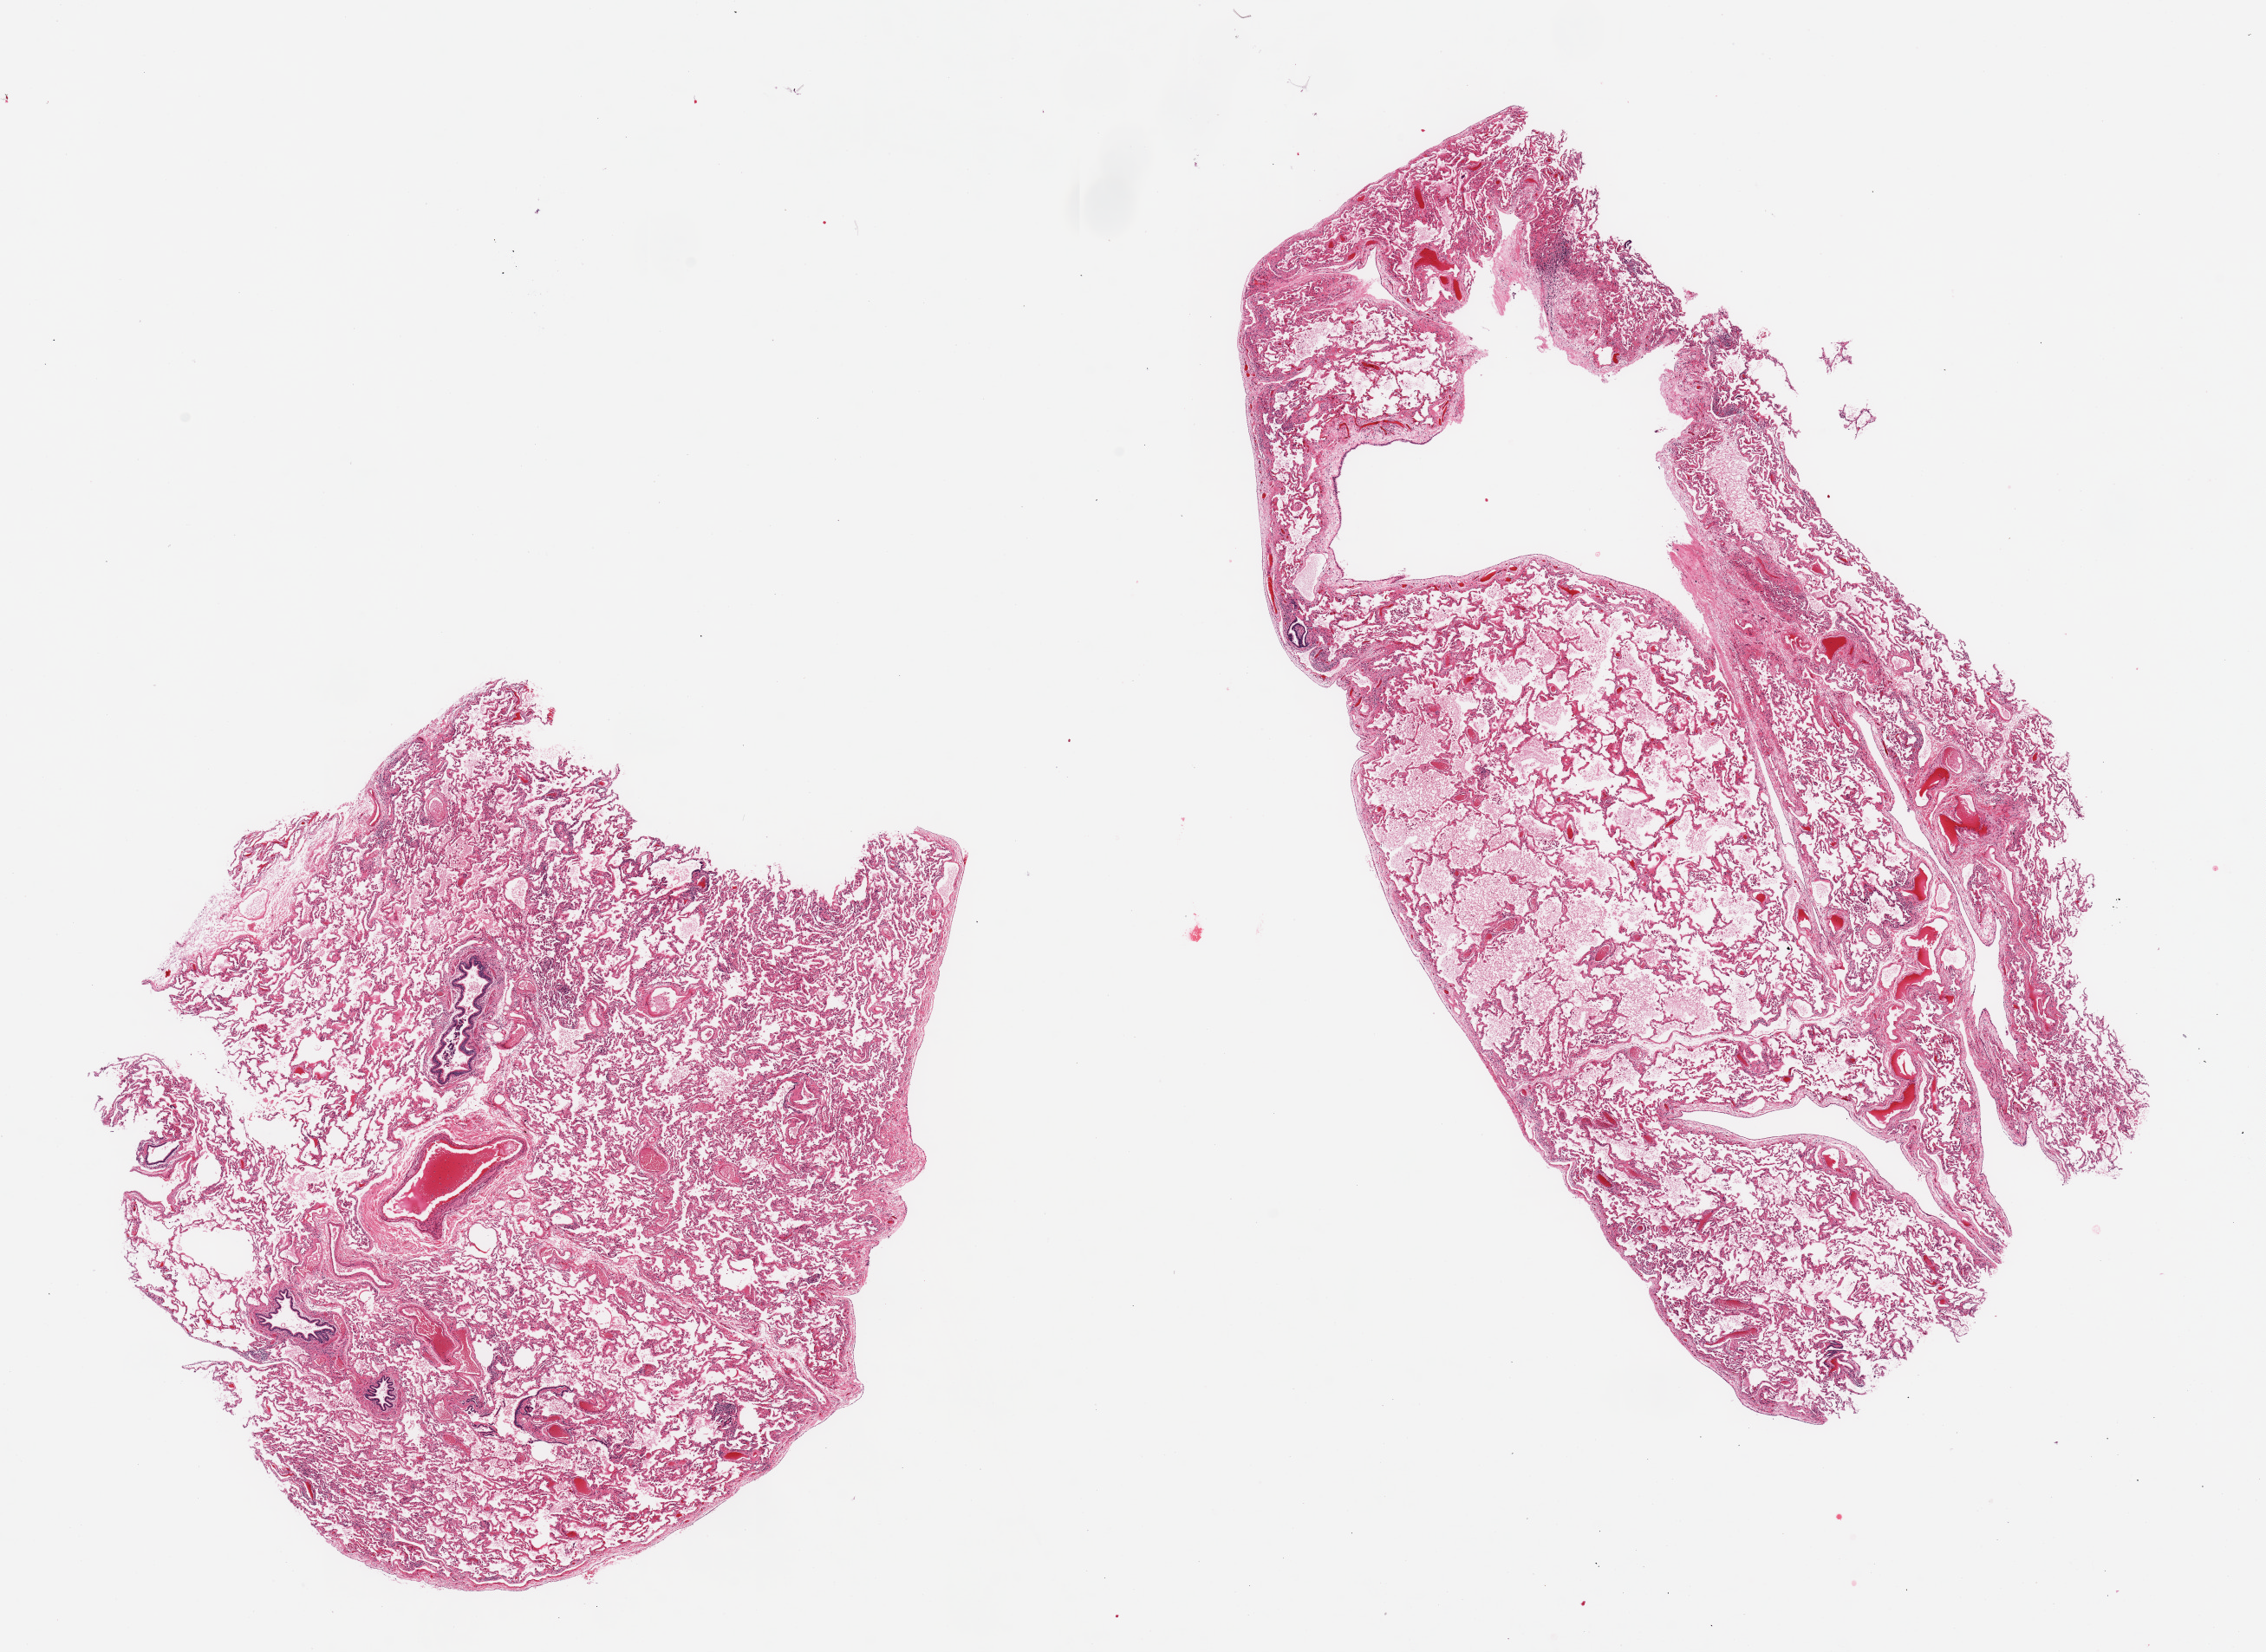
Whole-slide image, haematoxylin and eosin stain, a low-resolution overview of the entire scanned area, about 20.7 x 15.1 mm, PAXgene-fixed, paraffin-embedded tissue, section of lung (target tissue), donor tissue sample. Donor sex: female.
Reviewer comment on this tissue sample: 2 pieces; pulmonary edema; no fibrosis.